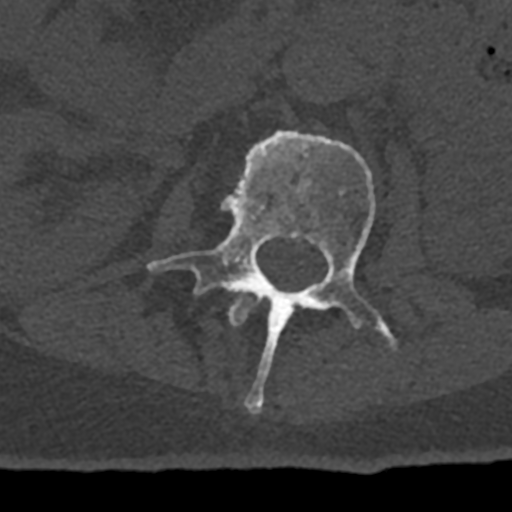
CT including the spine, one axial slice; slice 383 of 797 in the series (ordered by position); reconstruction kernel Br40s/3; bone window (W 1800 / L 400 HU); 512 × 512 image matrix. Patient: male, 74 years. Case-level facts recorded for this patient, not image findings: primary cancer: renal.
Annotated regions visible in this slice (semi-automatically segmented with operator editing):
- L1 vertebra: bounding box [x1, y1, x2, y2] px = [229, 291, 253, 326]
- L2 vertebra: [147, 130, 397, 414]